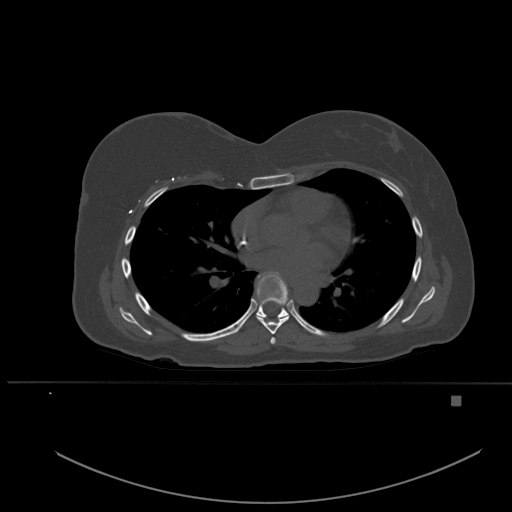
CT including the spine, one axial slice. Slice 344 of 651 in the series (ordered by position). Bone window (W 1800 / L 400 HU). 1.5 mm slice thickness. 512 × 512 image matrix, field of view 443 × 443 mm. Female patient, age 49 years. From the clinical record (not read from this slice): primary cancer: breast; vertebrae with lytic lesions (as recorded): L3, T12, L4.
Structures marked on this image (semi-automatic segmentation, software-assisted and operator-edited):
- T5 vertebra: box from (x=270, y=337) to (x=276, y=344) px
- T6 vertebra: (x=257, y=272)–(x=290, y=334)
- T7 vertebra: (x=256, y=275)–(x=288, y=319)